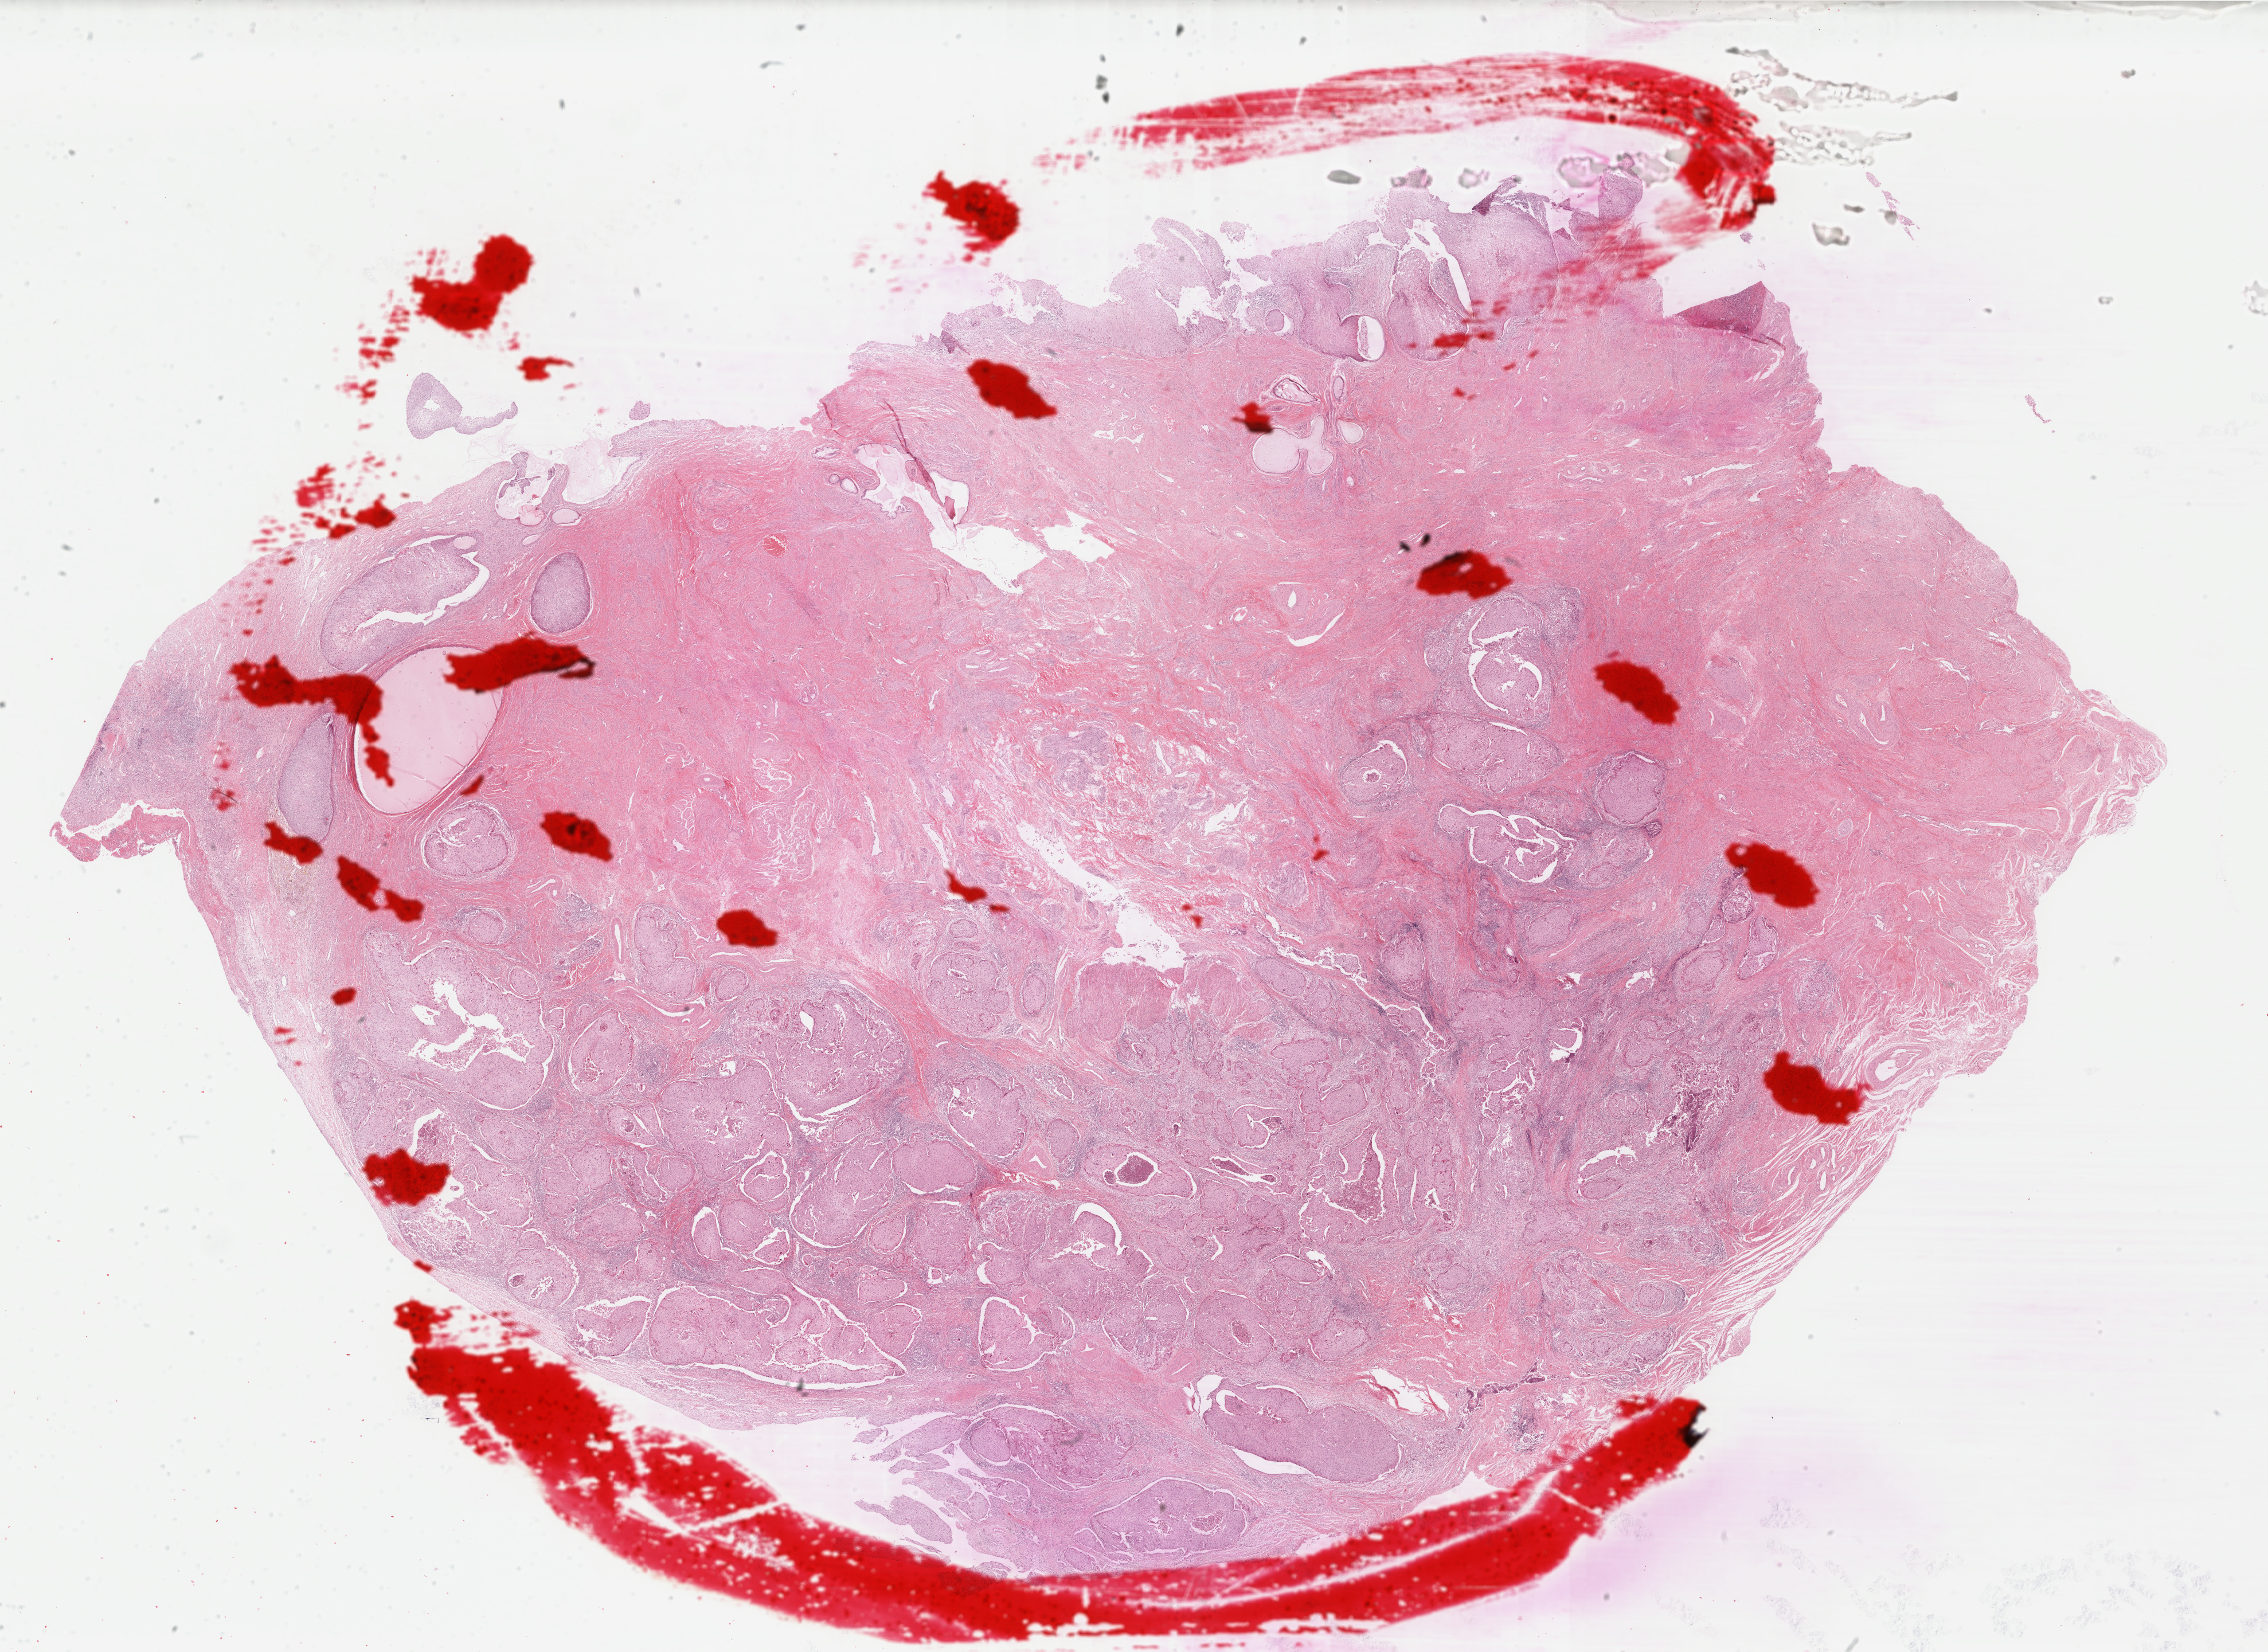
Digitized H&E-stained tissue section (whole slide), a low-resolution overview of the entire scanned area, about 31.4 x 22.9 mm (from a 40x scan), formalin-fixed paraffin-embedded (FFPE) diagnostic section, sample: primary tumour, cervix. Patient: female, age at initial diagnosis 57 years. Histologic grade: G2 (moderately differentiated).
- pathologic diagnosis: Squamous cell carcinoma, NOS (cervix uteri)
- FIGO stage: II